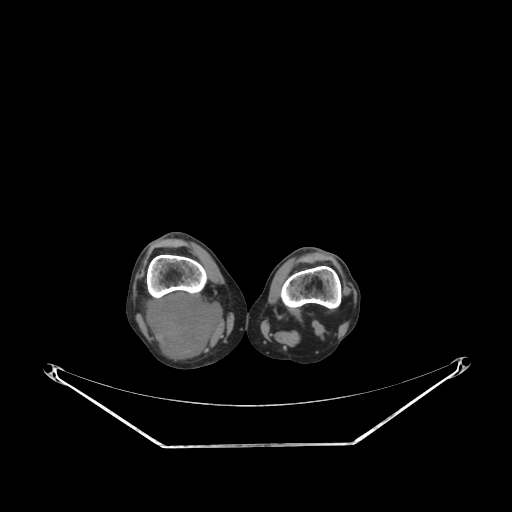
CT of an extremity soft-tissue mass (from a PET/CT study), one axial slice; slice 175 of 267 in the series (ordered by position); 140 kVp; soft-tissue window (W 400 / L 40 HU); 3.75 mm slice thickness; 512 × 512 image matrix, field of view 500 × 500 mm. Female patient. Case-level facts recorded for this patient, not image findings: histological type: liposarcoma; site of the primary tumour: right thigh.
Structures marked on this image (expert contour drawn on MRI and transferred to this co-registered scan by the dataset authors):
- gross tumour volume (mass): bounding box (x1, y1, x2, y2) in pixels: (144, 291, 225, 360)